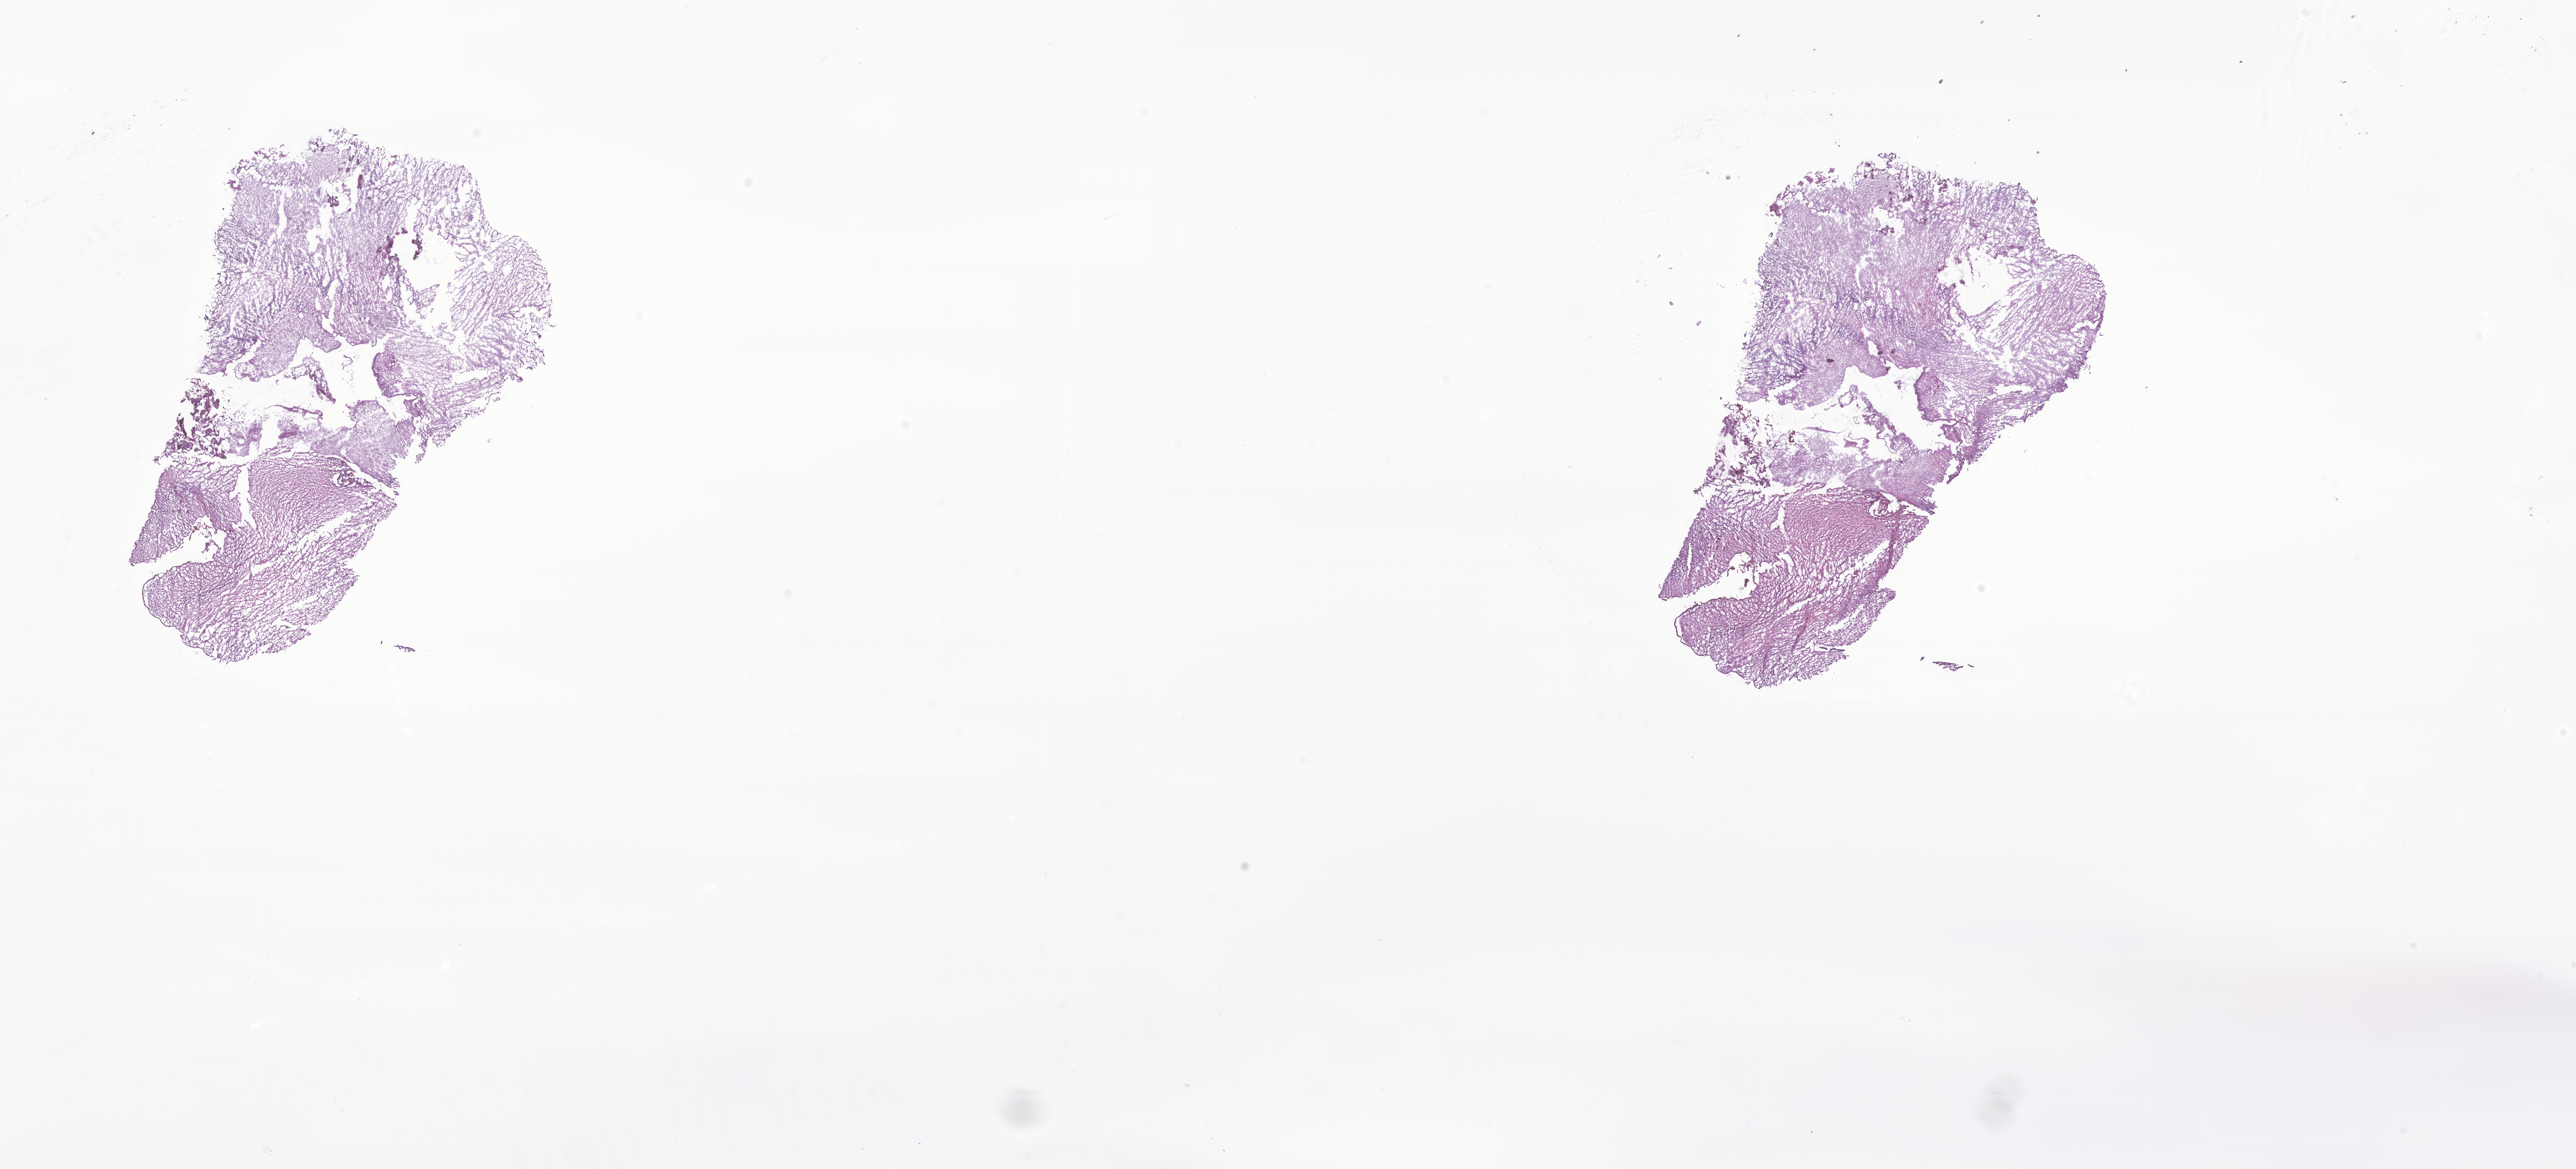
Digitized haematoxylin and eosin-stained section of tumor tissue from the cerebellum, whole scanned area (about 37.0 x 16.8 mm) shown as a low-resolution overview. Frozen section. Male patient, age 145 months (12 years 1 month).
* diagnosis: Pilocytic astrocytoma